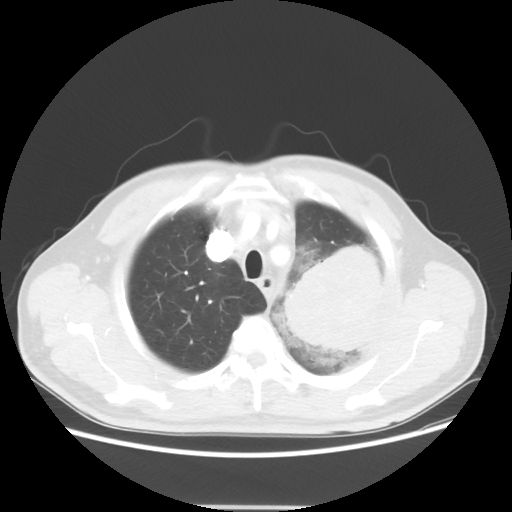
Chest CT, one axial slice. Position 45 of 53 along the scan axis. Reconstruction kernel STANDARD. 100 kVp. Lung window (W 1500 / L -600 HU). 5 mm slice thickness. 512 × 512 image matrix. Patient: male, 60 years. From the clinical record (not read from this slice): clinical TNM (as recorded): T4 N1 M1a; histopathological grade: G3.
Structures marked on this image (rectangle marked by the reading radiologist):
- lung tumour (recorded histology: large cell carcinoma): bounding box [x1, y1, x2, y2] px = [289, 239, 388, 362]